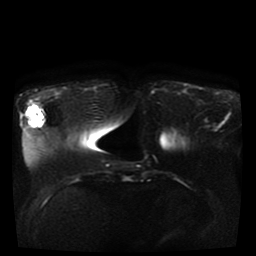
Breast MRI, one axial slice; position 14 of 41 along the scan axis; diffusion-weighted series; image 2 of 4 stored at this slice position (different b-values; order by instance number); 1.5 T; 5 mm slice thickness; 256 × 256 image matrix, field of view 330 × 330 mm. Female patient.
Structures marked on this image (manually delineated by an expert):
- tumour on diffusion-weighted imaging: bounding box (x1, y1, x2, y2) in pixels: (26, 106, 43, 126)